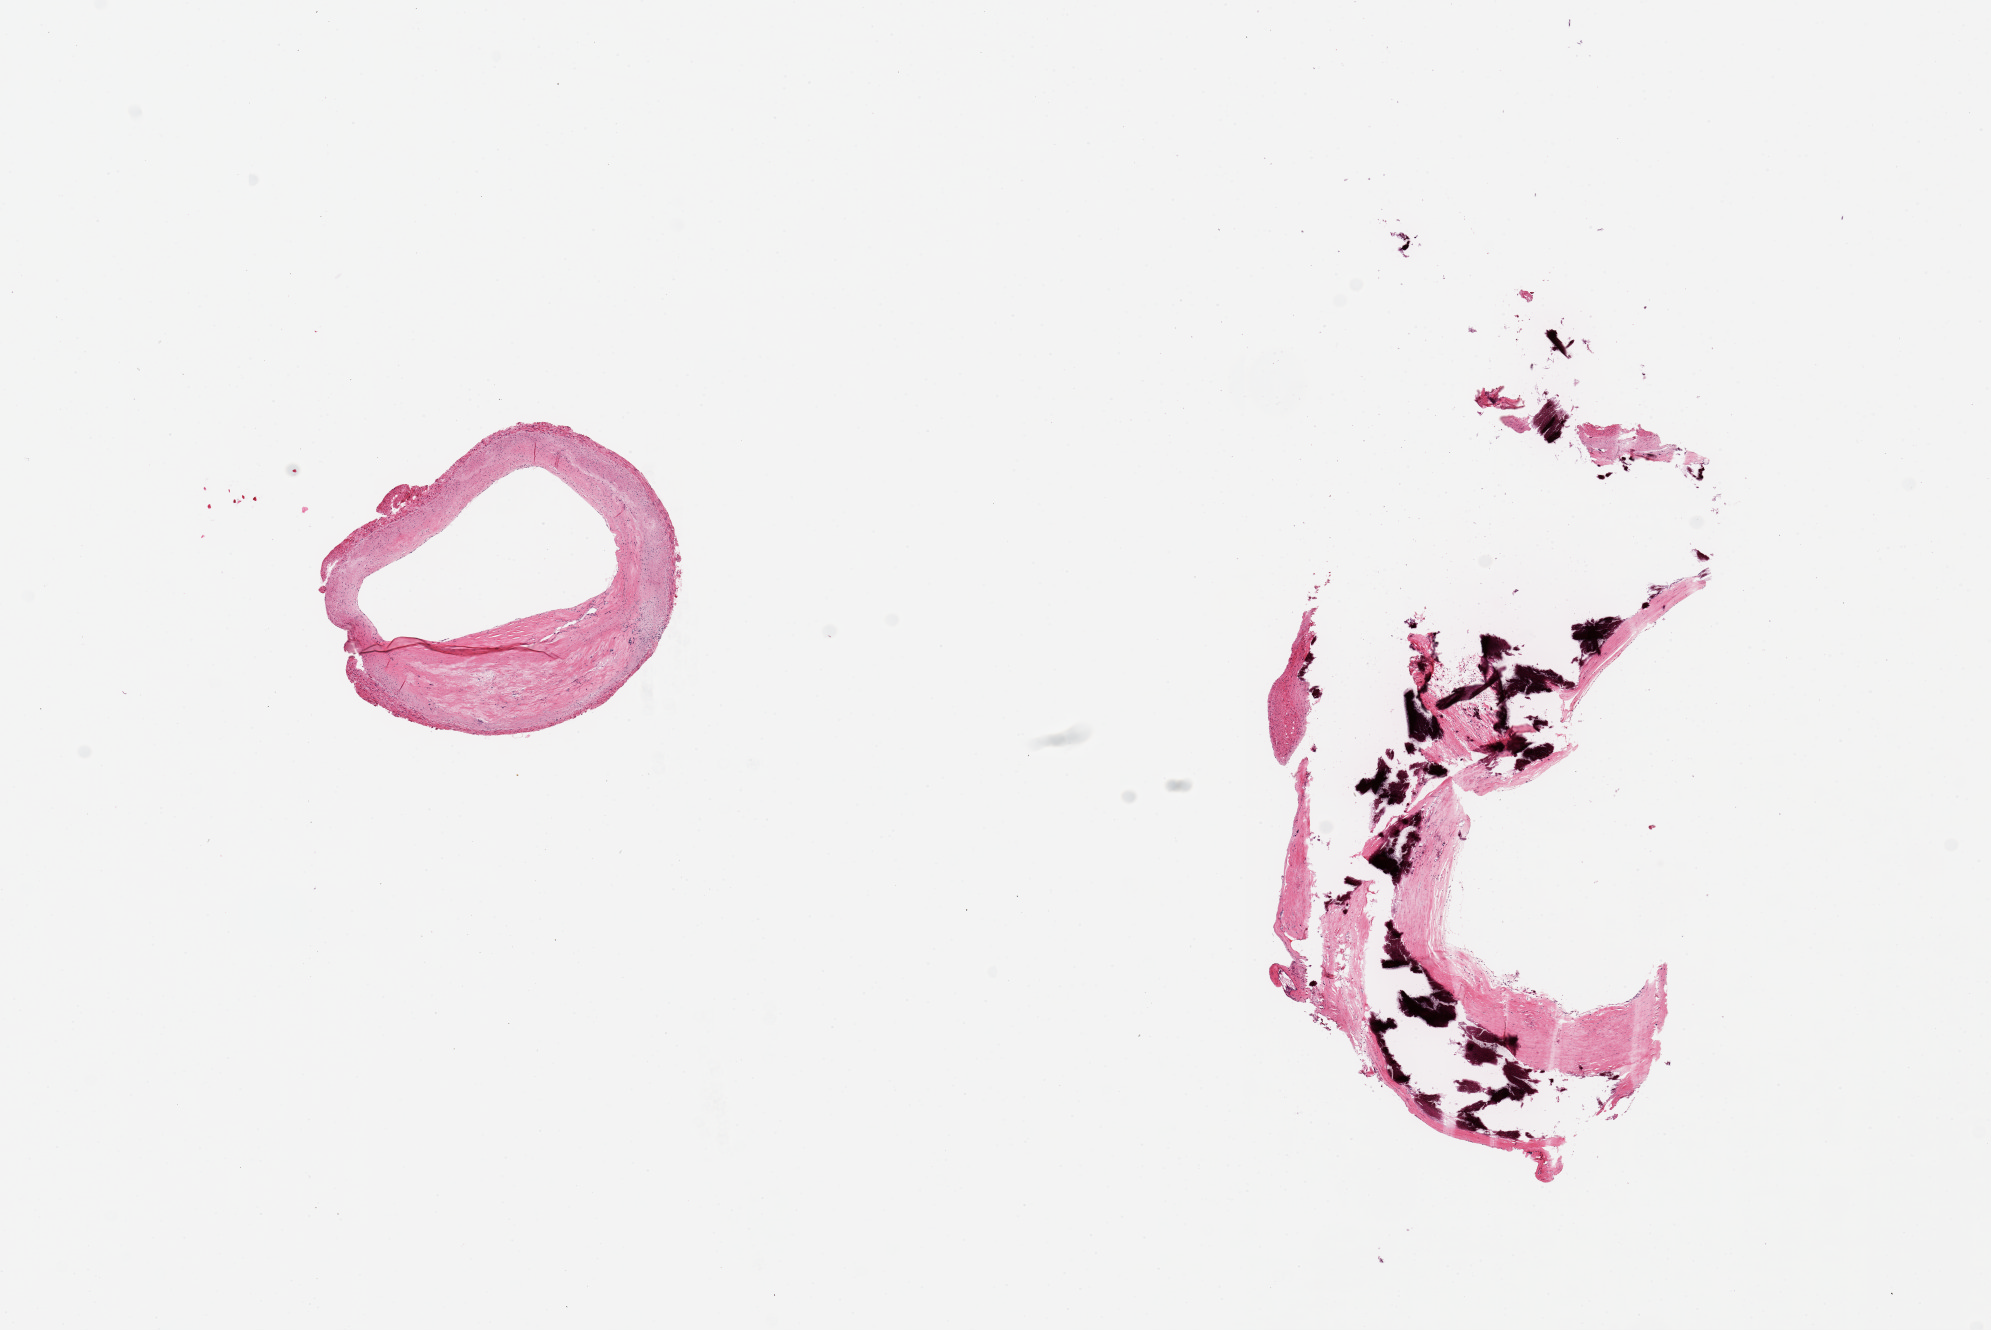
Haematoxylin and eosin whole-slide image — whole scanned area (about 15.8 x 10.5 mm) shown as a low-resolution overview, PAXgene-fixed paraffin-embedded (PFPE) section, sampled site (target tissue): coronary artery, tissue donor sample.
- reviewer comment on this tissue sample: 2 pieces ~2.5mm d. One markedly calcified, with shatter